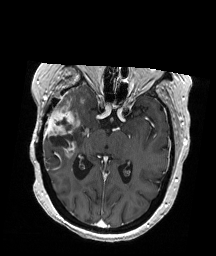
Brain MRI from a brain-tumour surgery series, one axial slice. Slice 111 of 192 in the series (ordered by position). T1-weighted post-contrast. 1 mm slice thickness. 216 × 256 image matrix, field of view 211 × 250 mm. From the clinical record (not read from this slice): histopathology: Glioblastoma; WHO grade: 4; IDH mutation: no; tumour location: Right Temporal.
Structures marked on this image (expert manual segmentation):
- tumour: bounding box [x1, y1, x2, y2] px = [44, 87, 90, 158]